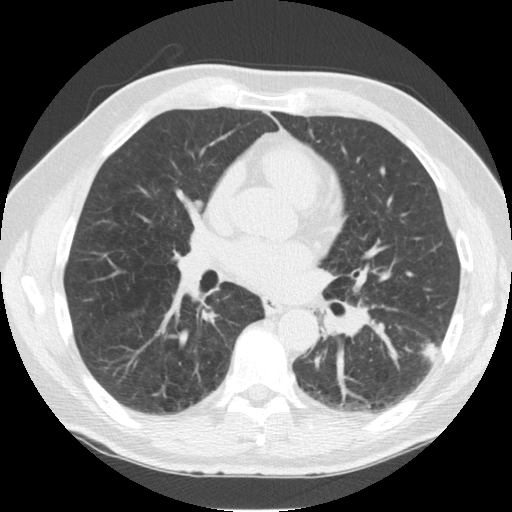
Chest CT (low-dose screening protocol), one axial image. Third annual screen. Lung window (W 1500 / L -600 HU). 512 × 512 image matrix, field of view 344 × 344 mm. Male participant, aged 57 years at enrolment. Former smoker at enrolment.
Expert reader's lesion annotation, bounding box <407,325,450,372> (left, top, right, bottom; pixels). Screening reader's record for this exam (one nodule recorded; not confirmed to be the boxed lesion): non-calcified nodule or mass ≥4 mm, left lower lobe, 13 × 12 mm, spiculated (stellate) margins, soft tissue attenuation, pre-existing on the prior screen: yes; interval growth: yes. Later outcome: lung cancer diagnosed 49 days after this screen — non-small cell carcinoma, left lower lobe, stage IV (AJCC 6th edition), 13 mm at pathology.